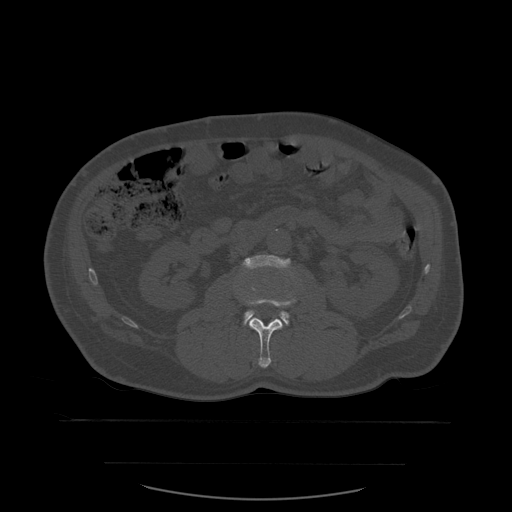
CT including the spine, one axial slice; position 209 of 590 along the scan axis; bone window (W 1800 / L 400 HU); 1.25 mm slice thickness; 512 × 512 image matrix, field of view 479 × 479 mm. Patient age 71 years. From the clinical record (not read from this slice): primary cancer: lung; vertebrae with lytic lesions (as recorded): T1, T2, L5, S1.
Structures marked on this image (semi-automatically segmented with operator editing):
- L2 vertebra: box from (x=243, y=287) to (x=296, y=368) px
- L3 vertebra: (x=243, y=255)–(x=292, y=324)